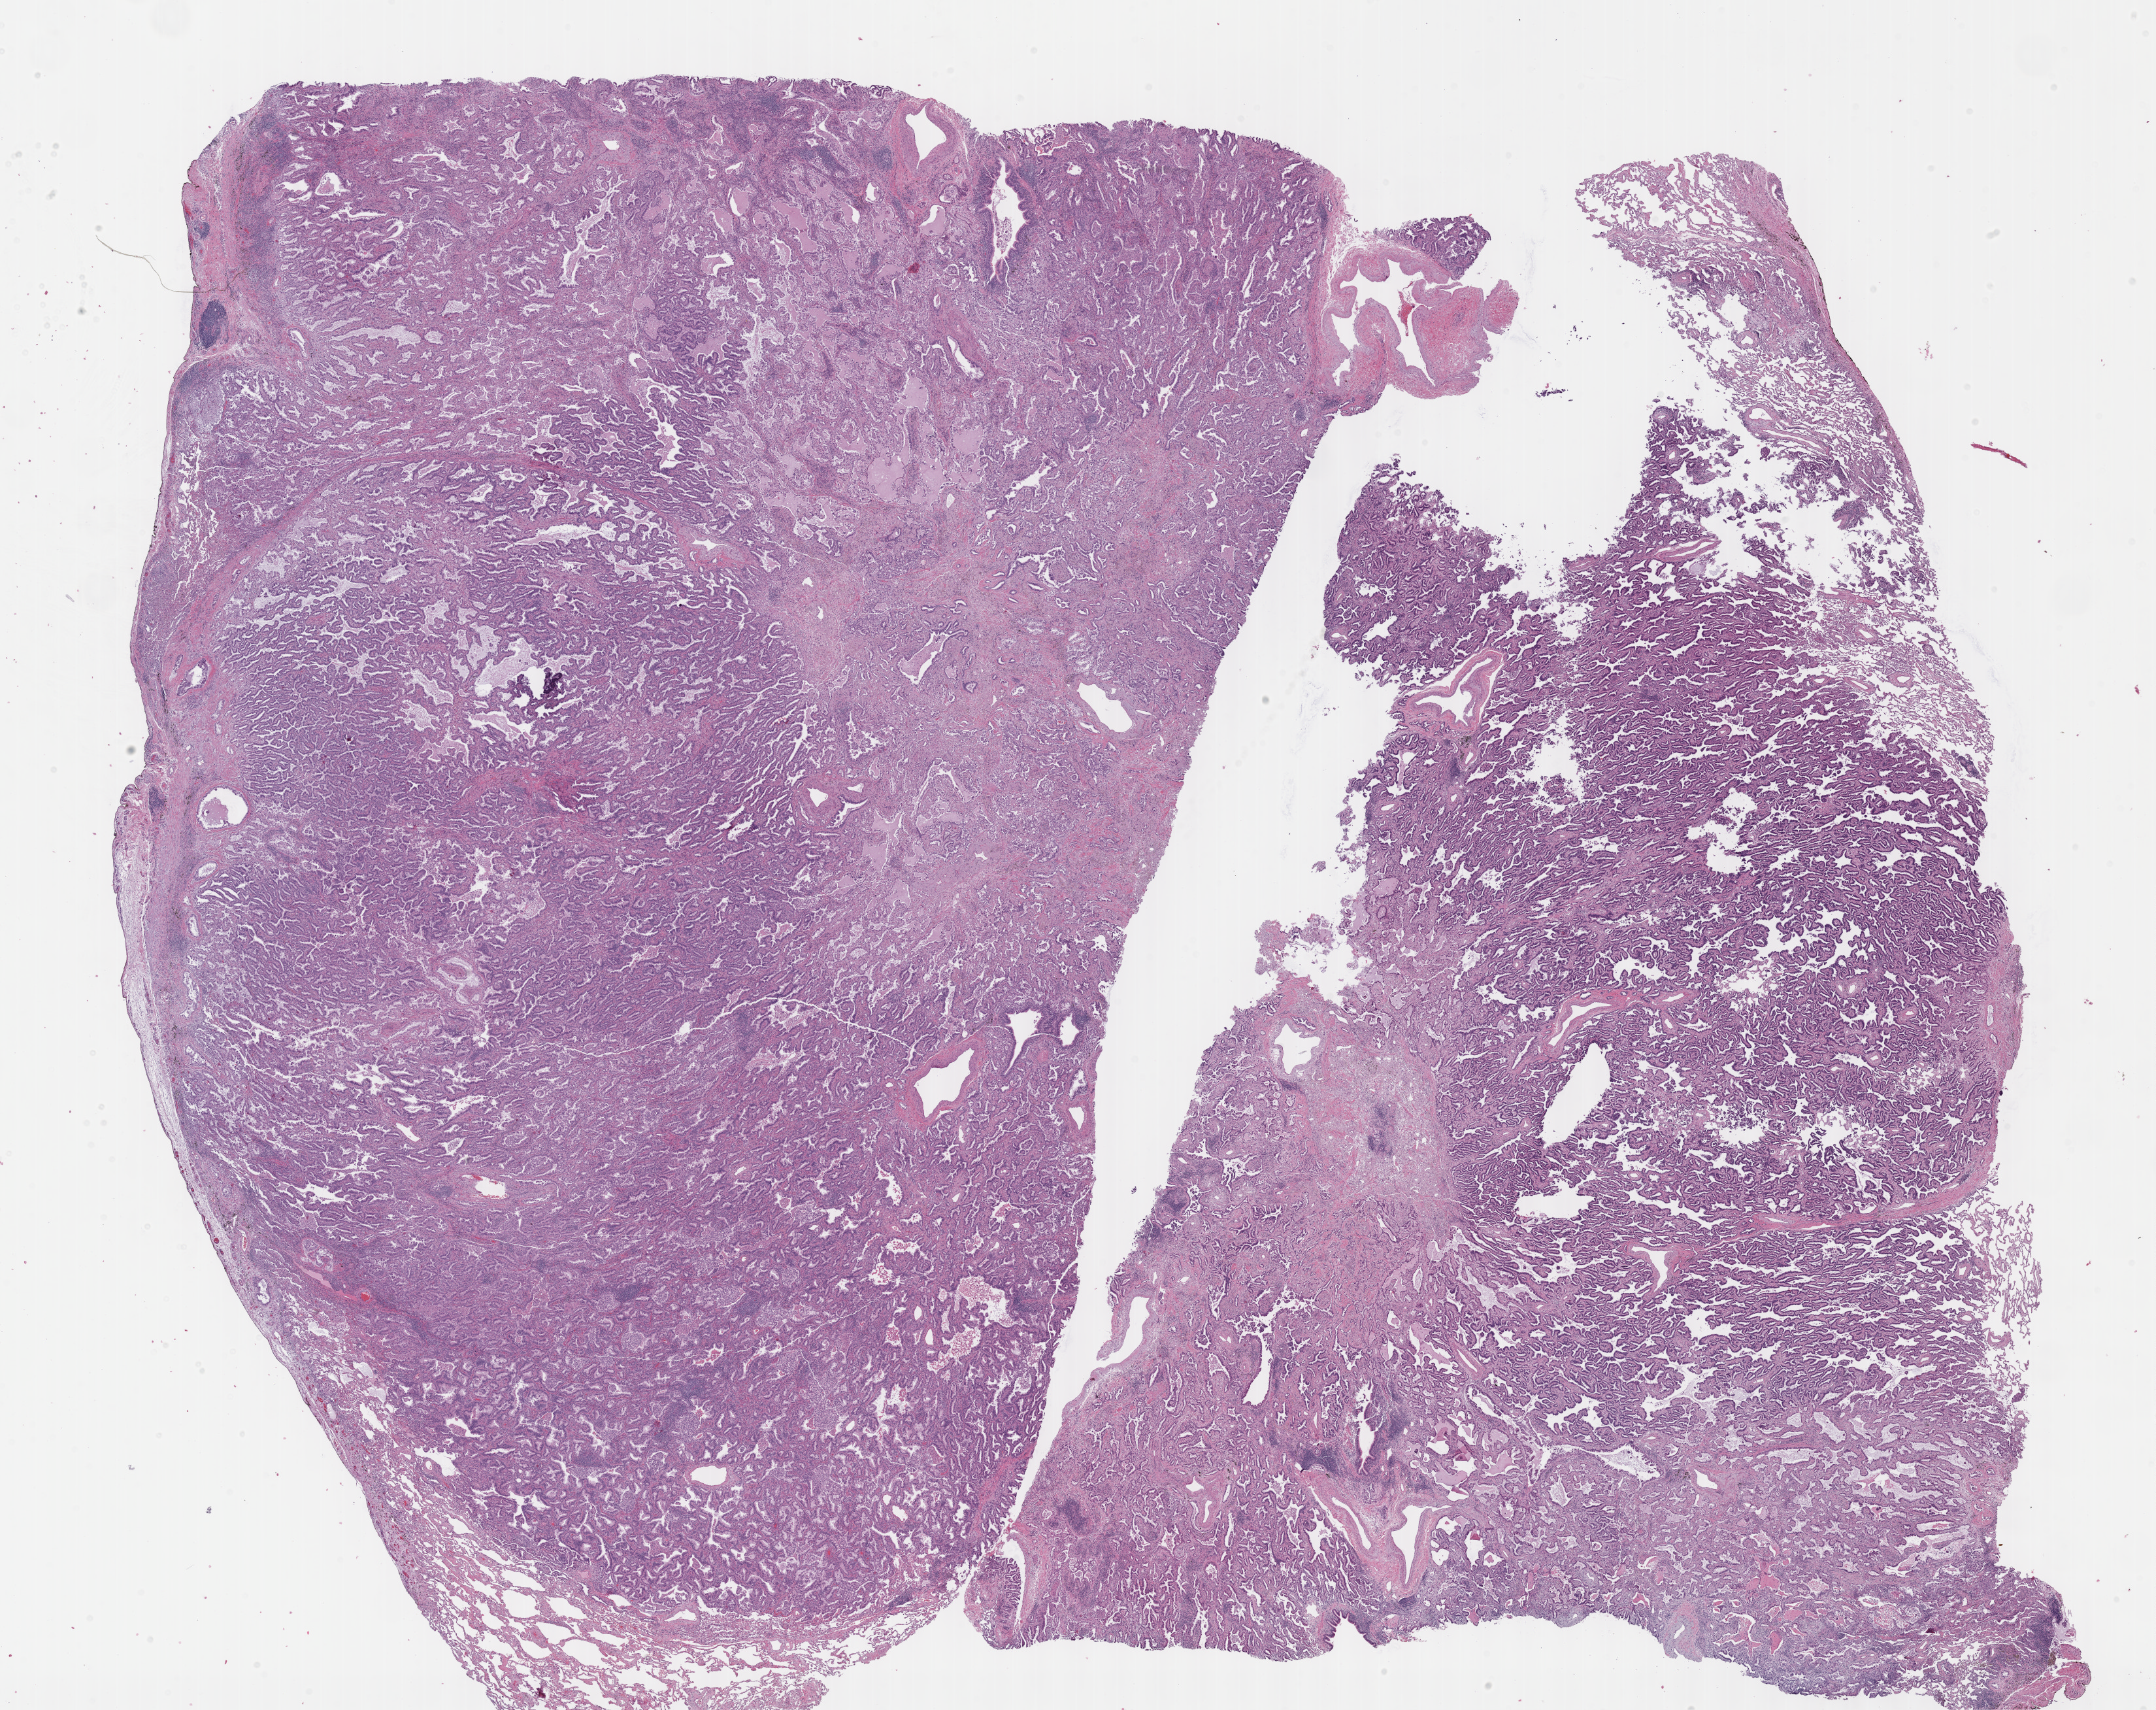
Hematoxylin and eosin (H&E) stained whole-slide image — low-resolution overview of the scanned area, about 26.7 x 21.1 mm. FFPE section. Lung, primary tumour sample. Patient: female, age at initial diagnosis 76 years.
• AJCC pathologic stage: IIIA
• diagnosis: Adenocarcinoma, NOS